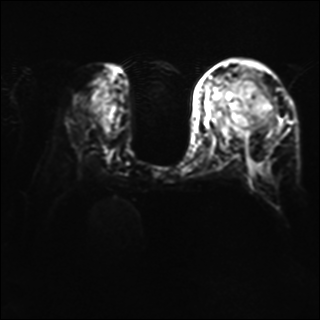
Breast MRI, one axial slice; diffusion-weighted series; image 2 of 4 stored at this slice position (different b-values; order by instance number); 1.5 T; 4 mm slice thickness; 320 × 320 image matrix, field of view 320 × 320 mm. Female patient.
Structures marked on this image (manually delineated by an expert):
- tumour on diffusion-weighted imaging: bounding box <233,81,262,119> (left, top, right, bottom; pixels)